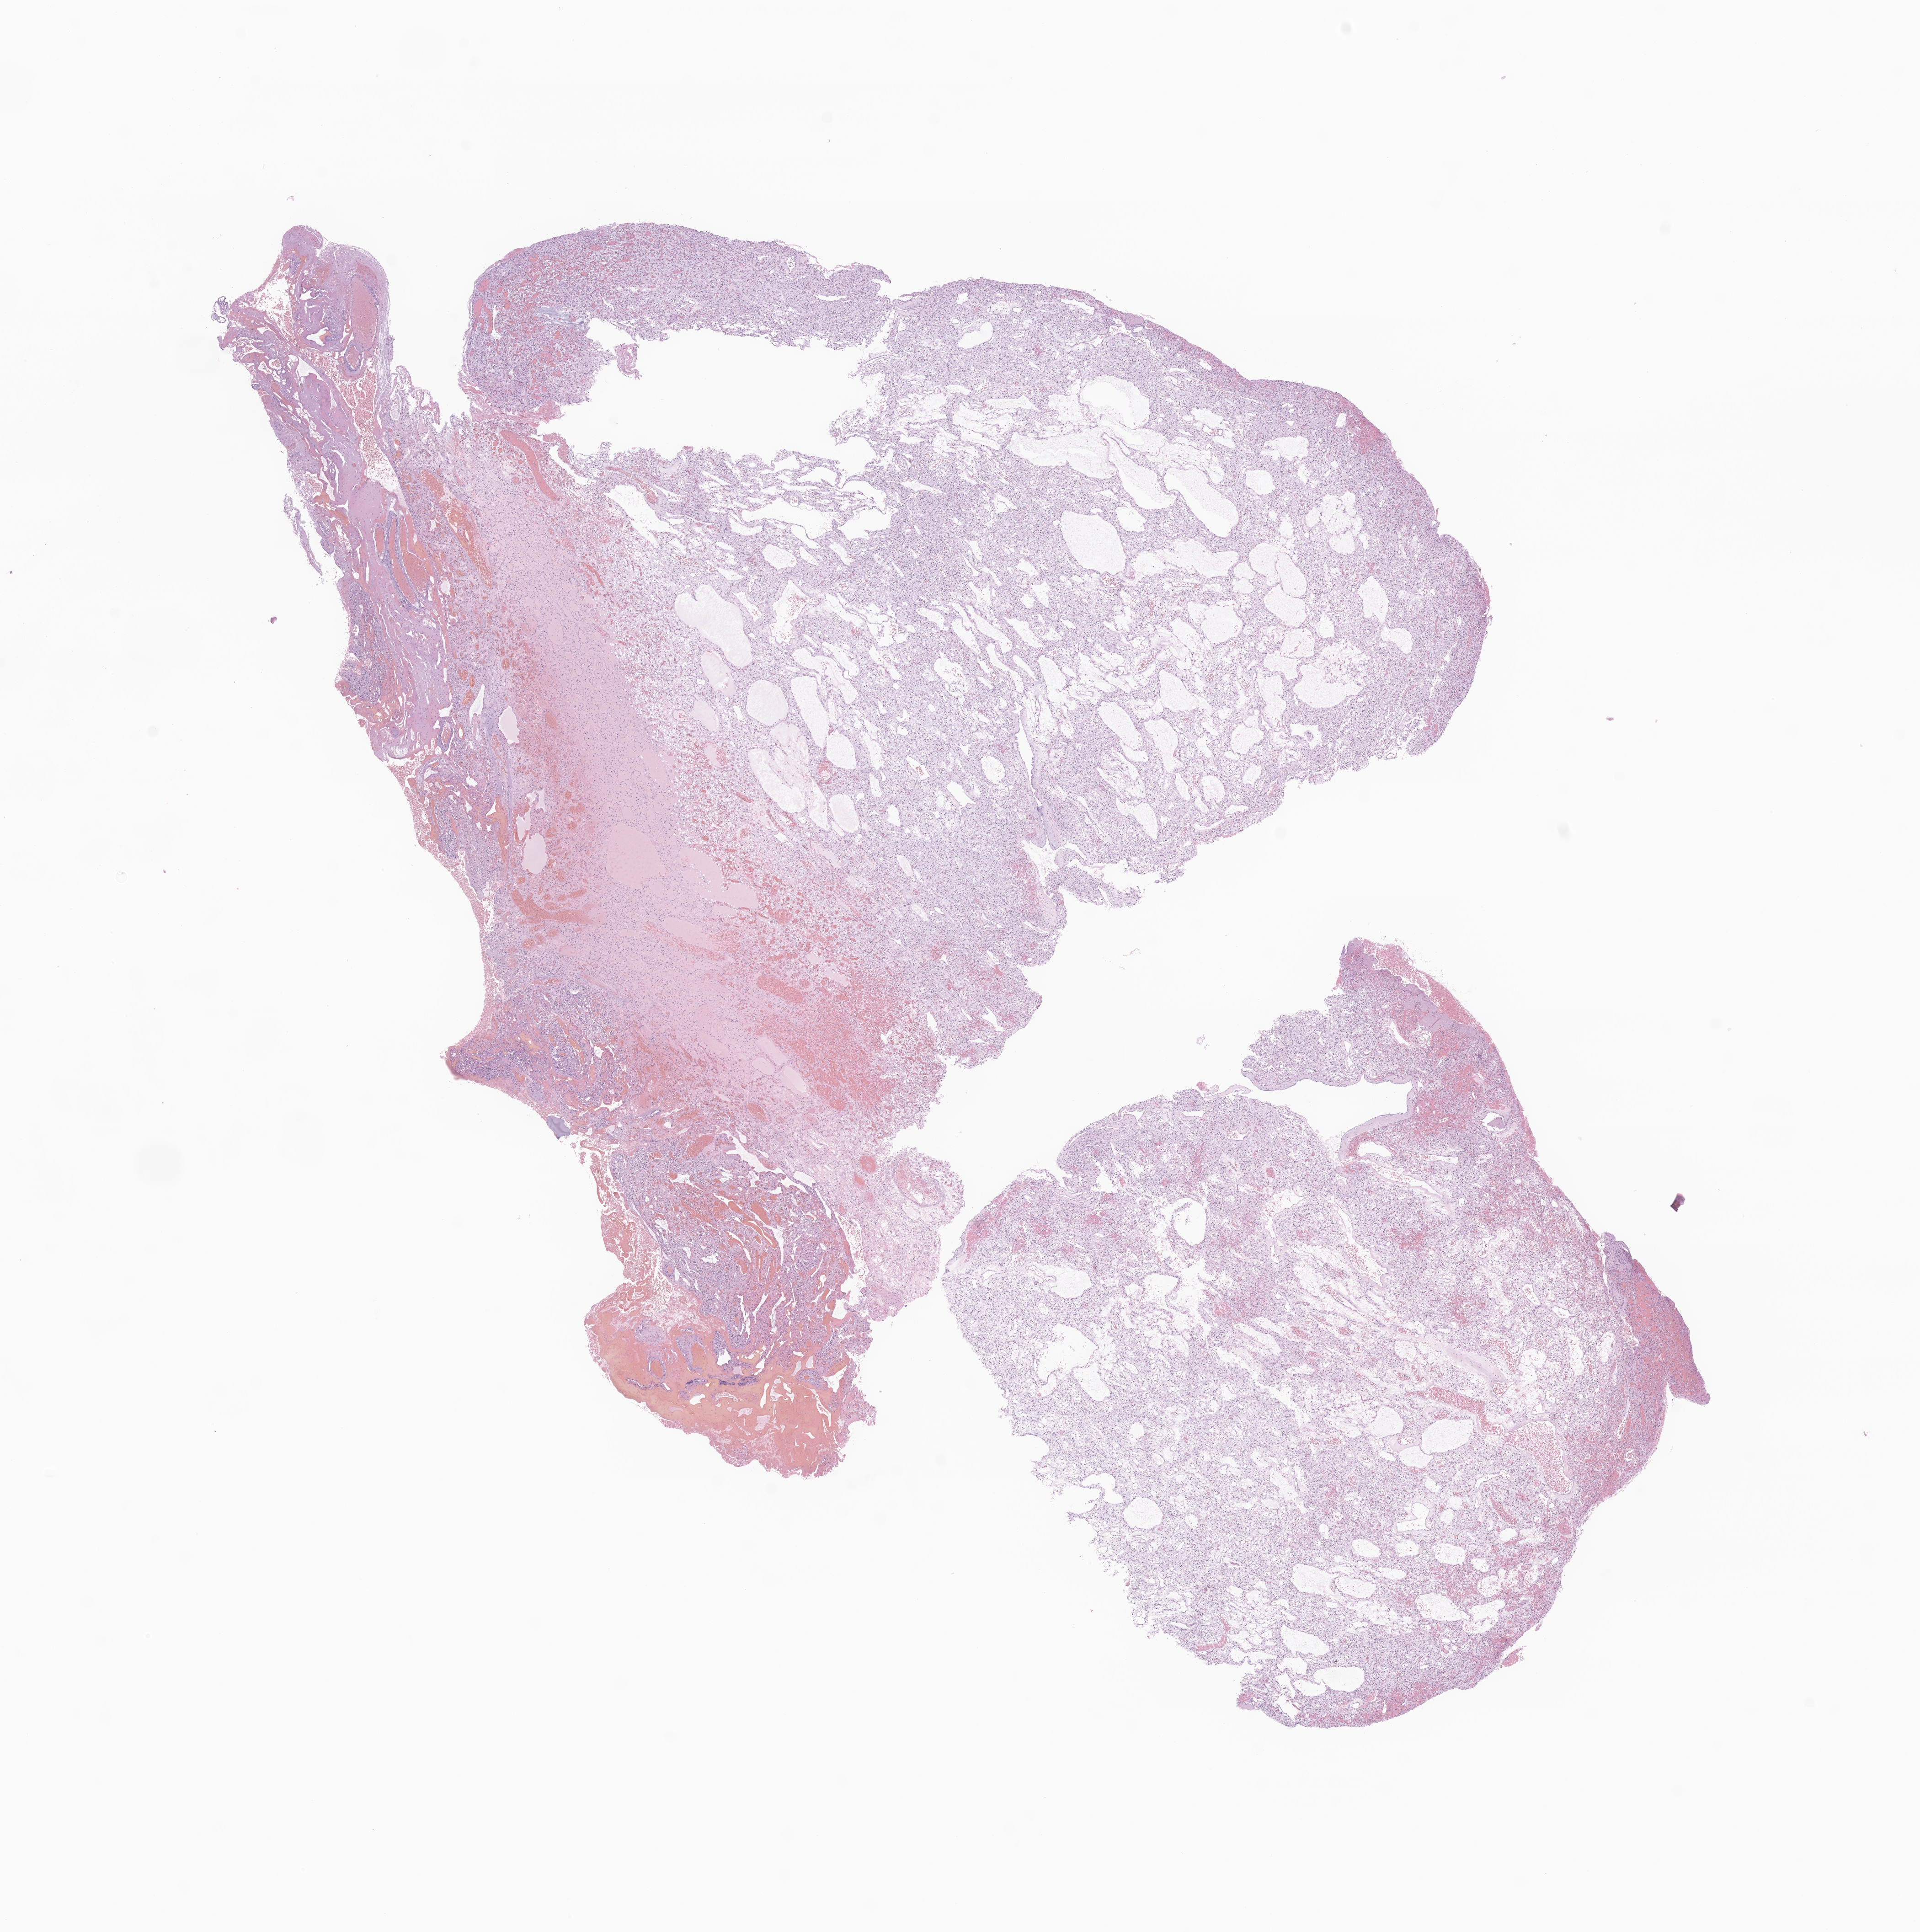
Whole-slide image, hematoxylin and eosin (H&E) stain of tumor tissue from the brain, shown as a low-resolution overview of the whole scanned area (about 17.7 x 17.8 mm), FFPE section. Patient: female, age 195 months (16 years 3 months).
Diagnosis (ICD-O-3 morphology term): Hemangioblastoma.